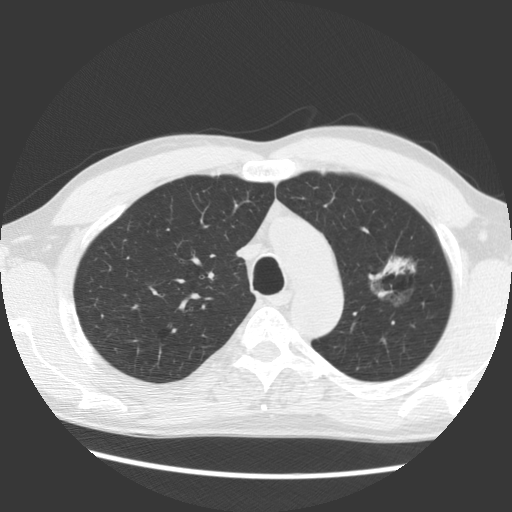
Chest CT (low-dose screening protocol), one axial image. First (baseline) screen. Lung window (W 1500 / L -600 HU). 2.5 mm slice thickness. Male participant, aged 61 years at enrolment. Former smoker at enrolment.
Lesion marked by an expert reader, bounding box <354,241,439,318> (left, top, right, bottom; pixels). The exam's reader record, not a measurement of the box and not confirmed to be the same lesion: non-calcified nodule or mass ≥4 mm, left upper lobe, 17 × 14 mm, soft tissue attenuation. Later outcome: lung cancer diagnosed 1061 days after this screen (after the third annual screen) — bronchiolo-alveolar adenocarcinoma, NOS, left upper lobe, well differentiated (G1), stage IB (AJCC 6th edition), 44 mm at pathology.